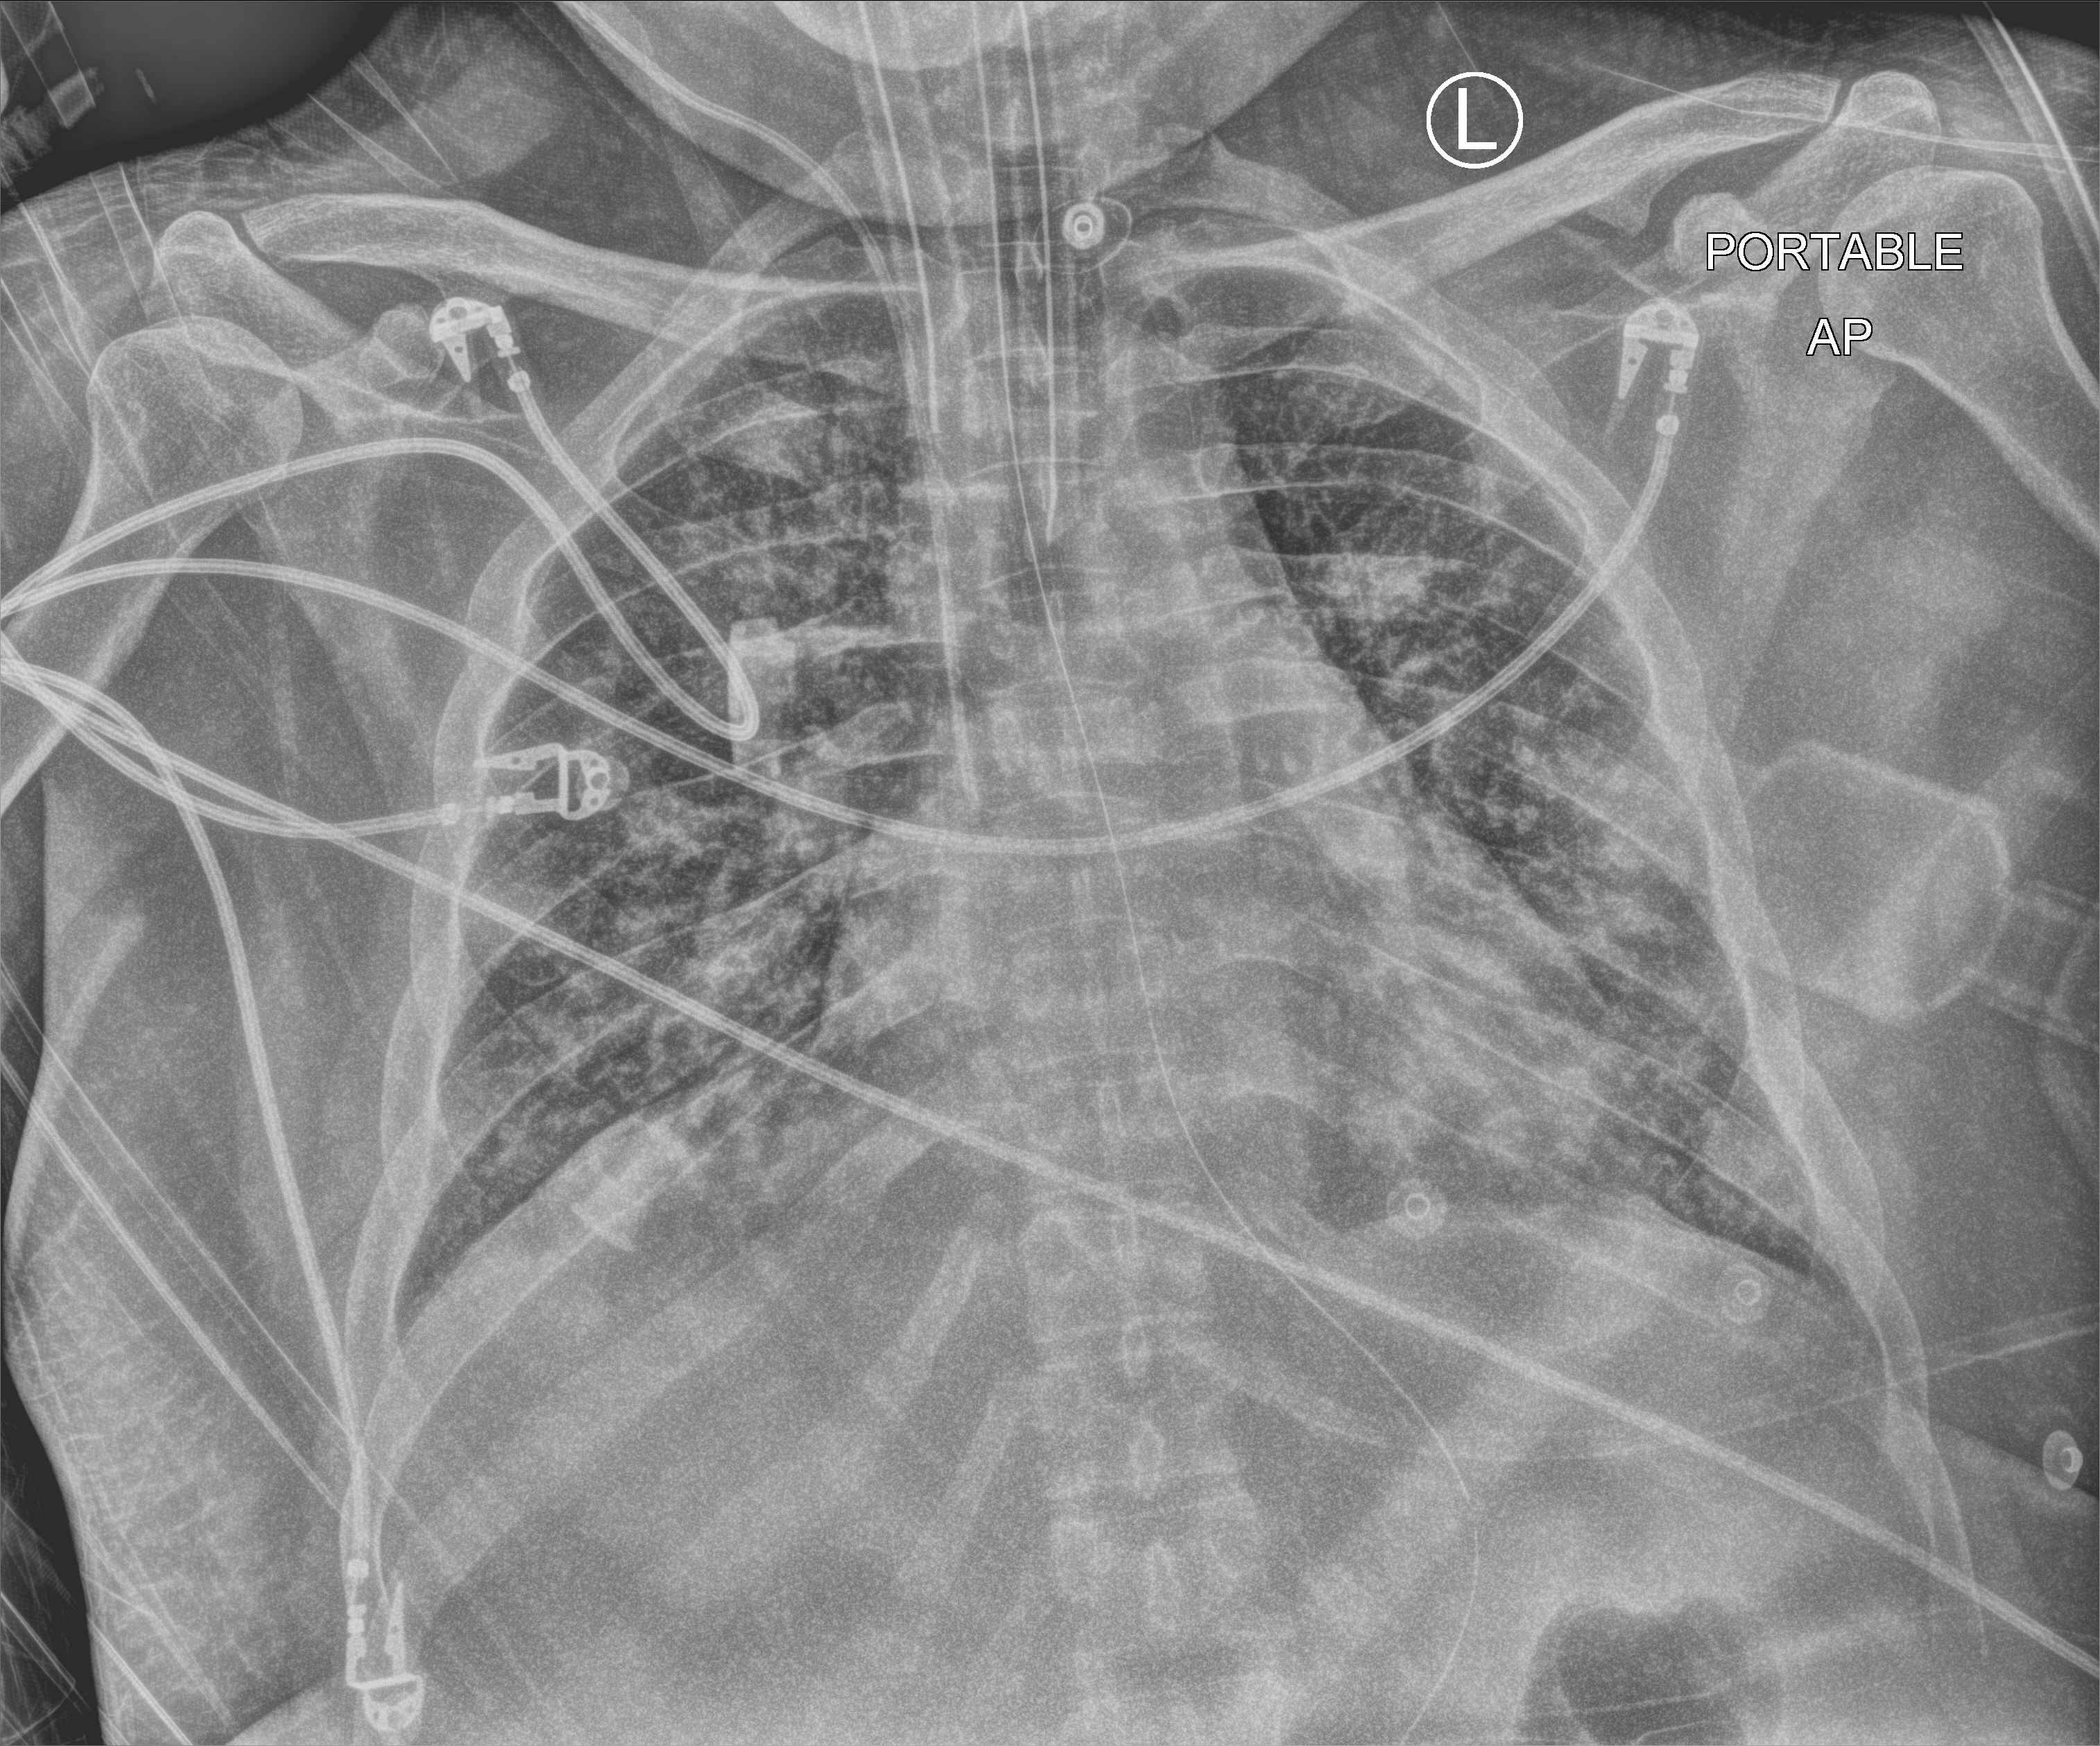
Portable chest radiograph, anteroposterior (AP) projection. Adult patient hospitalised with COVID-19, age 18–59 years.
Admission-level facts for this patient (not findings on this image; timing relative to this image not recorded): mechanically ventilated during this hospital stay: yes.